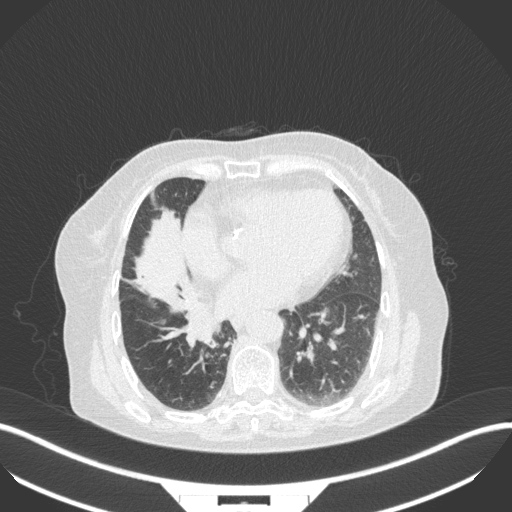
Chest CT, one axial slice; position 122 of 329 along the scan axis; 120 kVp; lung window (W 1500 / L -600 HU); 1 mm slice thickness; 512 × 512 image matrix. Female patient, age 75 years. From the clinical record (not read from this slice): clinical TNM (as recorded): T1b N0 M1a.
Outlined on this slice (rectangle marked by the reading radiologist):
- lung tumour (recorded histology: squamous cell carcinoma): bounding box (x1, y1, x2, y2) in pixels: (177, 314, 224, 348)